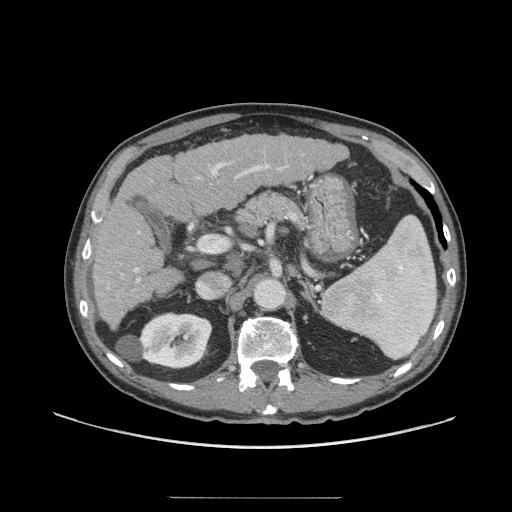
Contrast-enhanced abdominal CT (liver protocol), one axial slice. Soft-tissue window (W 400 / L 40 HU). 512 × 512 image matrix. Case-level facts recorded for this patient, not image findings: diagnosis: hepatocellular carcinoma (patient treated with transarterial chemoembolisation; whether this scan precedes or follows treatment is not stated here); TNM stage (as recorded): Stage-I; Child-Pugh class: A; tumour differentiation: well differentiated; tumour nodularity: uninodular.
Annotated regions visible in this slice (semi-automatic segmentation, software-assisted and operator-edited):
- liver parenchyma outside the tumour (the mass and vessels are separate outlines, so this box may not span the whole liver): bounding box <92,134,348,328> (left, top, right, bottom; pixels)
- liver vessels: <133,162,289,282>